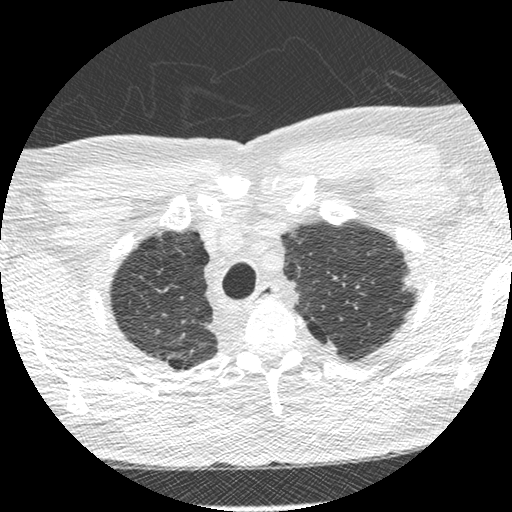
Low-dose screening chest CT, one axial slice; slice 242 of 275 in the series (ordered by position); reconstruction kernel STANDARD; lung window (W 1500 / L -600 HU); 1.25 mm slice thickness; 512 × 512 image matrix.
Annotated regions visible in this slice (manually delineated by an expert):
- lesion 1 (tumor, upper lobe of left lung): box from (x=403, y=276) to (x=411, y=291) px